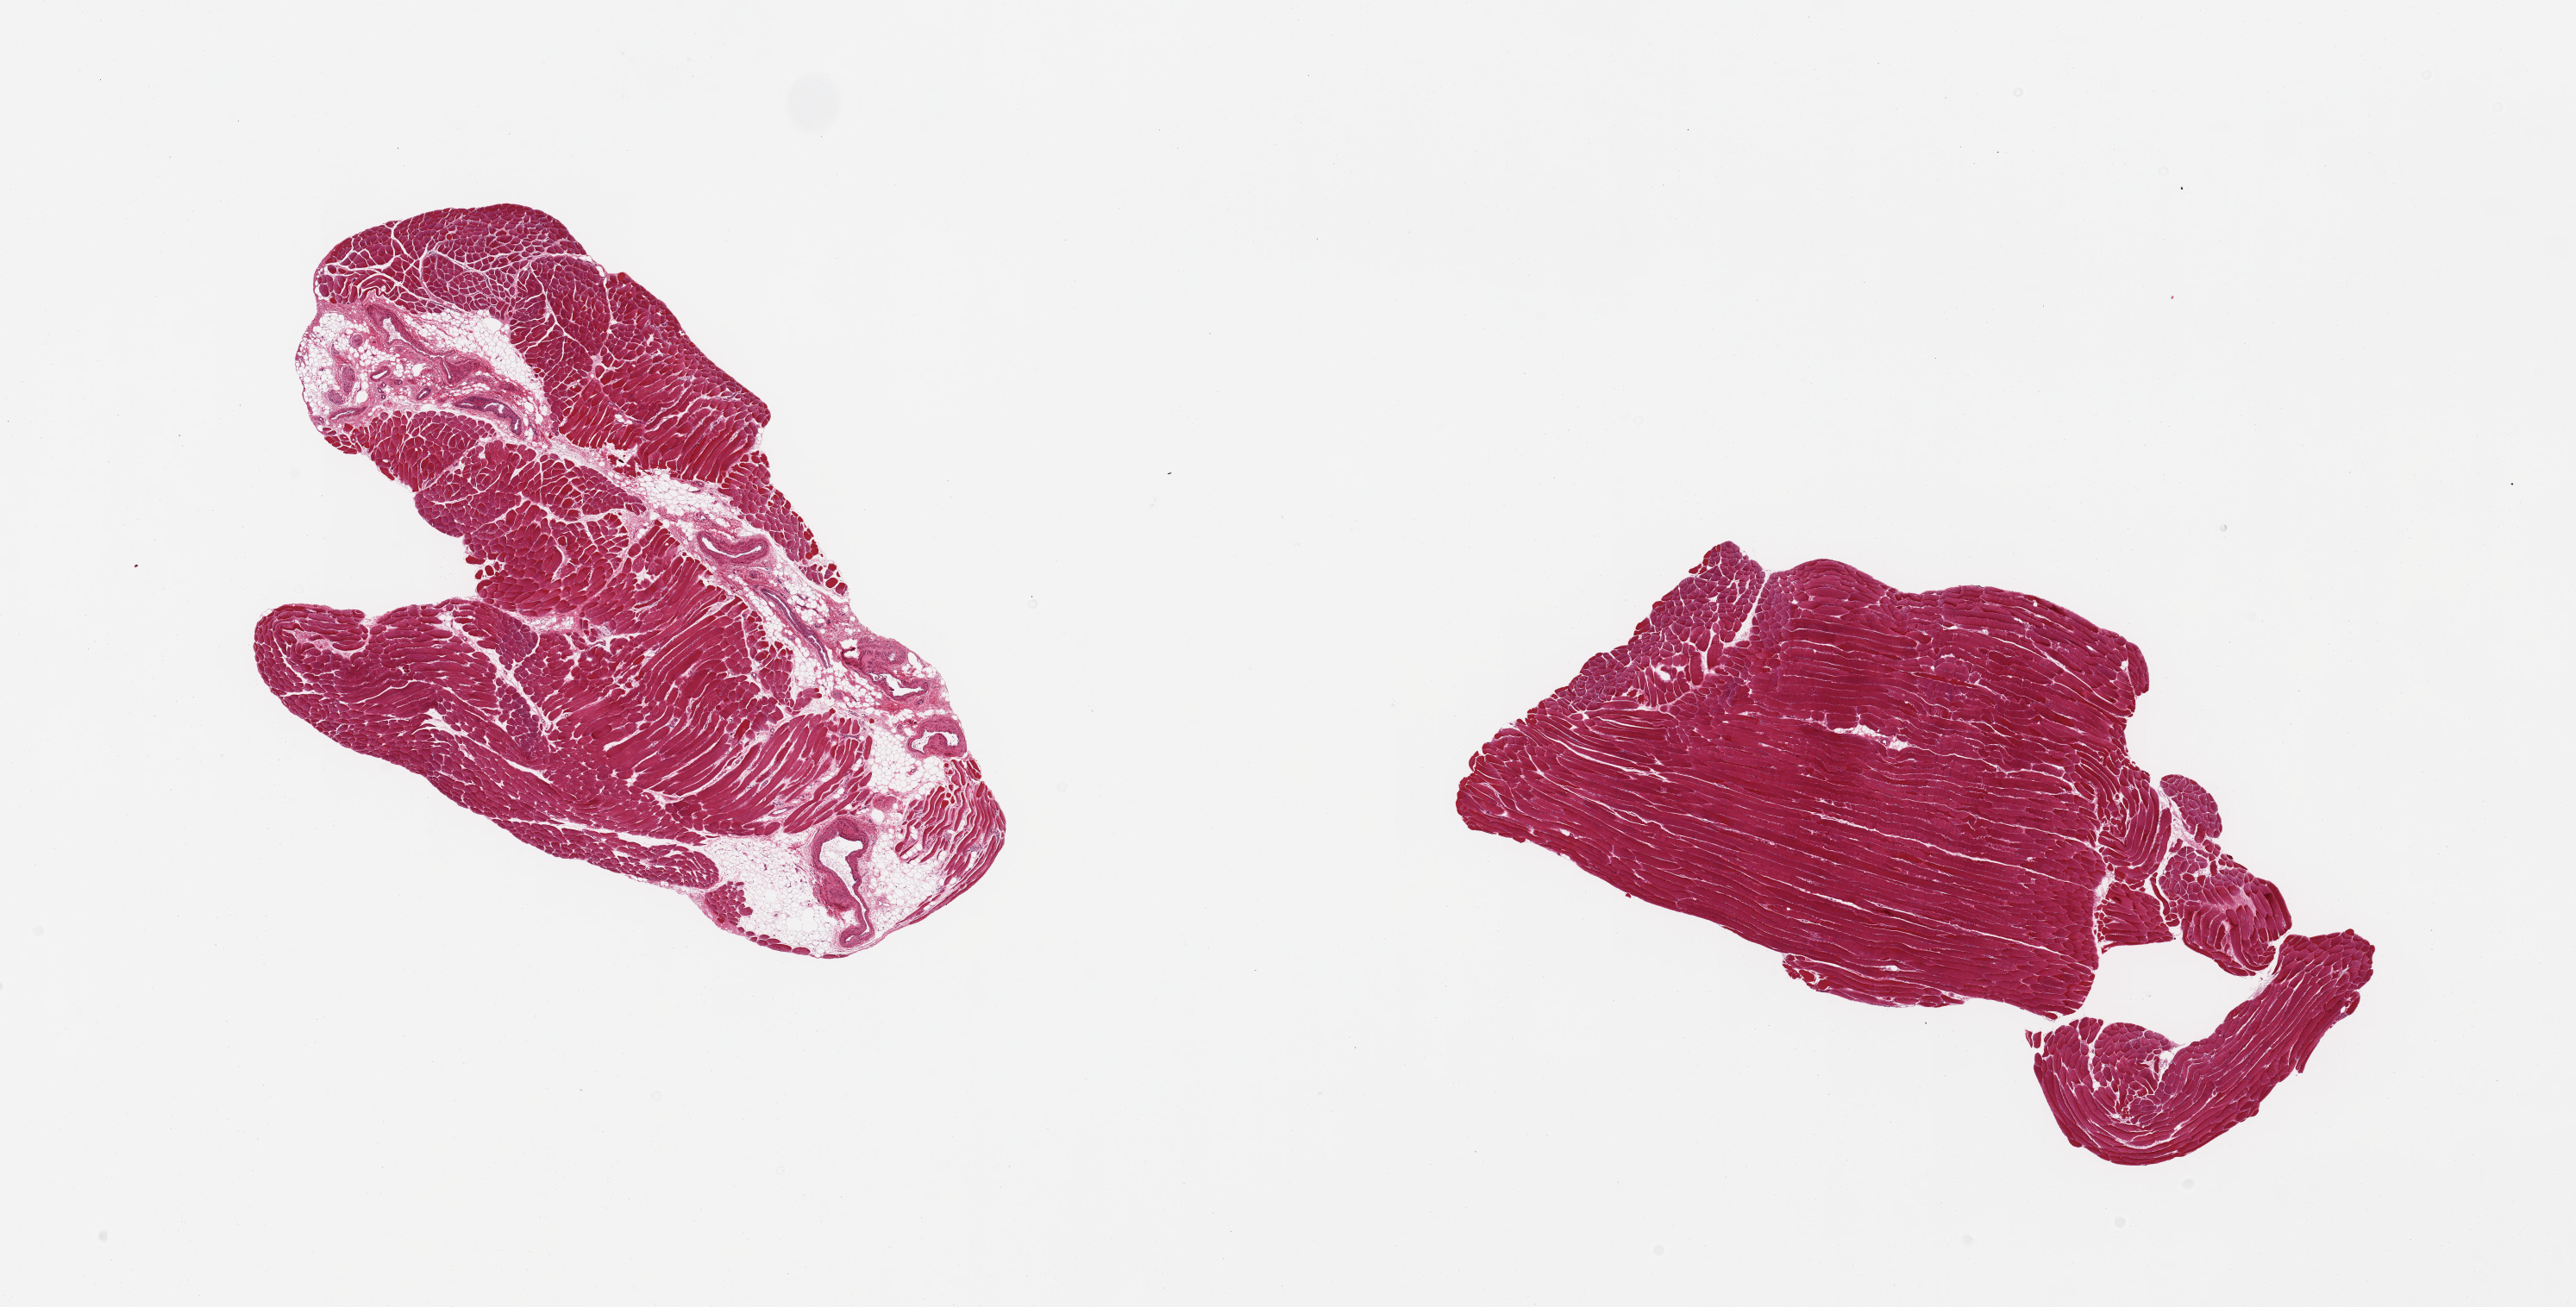
H&E whole-slide image — shown as a low-resolution overview of the whole scanned area (about 23.6 x 12.0 mm, from a 20x scan). PAXgene-fixed paraffin-embedded (PFPE) section. Section of skeletal muscle (target tissue). Donor tissue sample. Male donor.
Reviewer comment on this tissue sample: 2 pieces; 0% & 20% internal fat content.